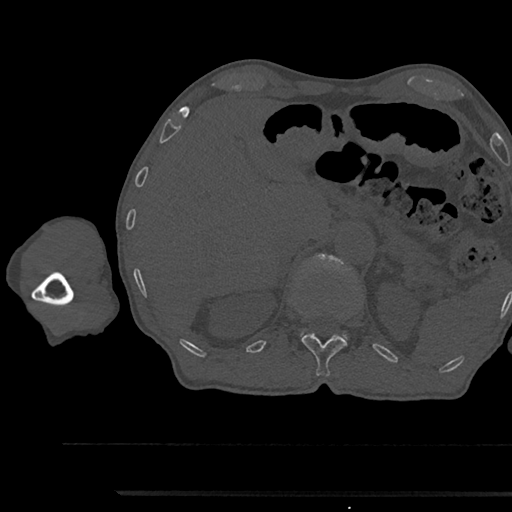
CT including the spine, one axial slice. Slice 689 of 797 in the series (ordered by position). Bone window (W 1800 / L 400 HU). 0.5 mm slice thickness. 512 × 512 image matrix, field of view 367 × 367 mm. Male patient, age 79 years. Case-level facts recorded for this patient, not image findings: primary cancer: prostate.
Outlined on this slice (semi-automatic segmentation, software-assisted and operator-edited):
- L1 vertebra: box from (x=300, y=254) to (x=355, y=340) px
- T12 vertebra: (x=302, y=333)–(x=348, y=377)